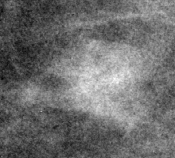
Region of interest cut from a scanned film mammogram (one marked finding), right breast, CC view, BI-RADS breast density category 1 (scale 1–4).
- Finding: mass, shape lymph node, margins circumscribed; BI-RADS assessment category 2; subtlety rating 4 on a 1 (subtle) to 5 (obvious) scale; benign; no additional work-up was recommended (benign without callback).